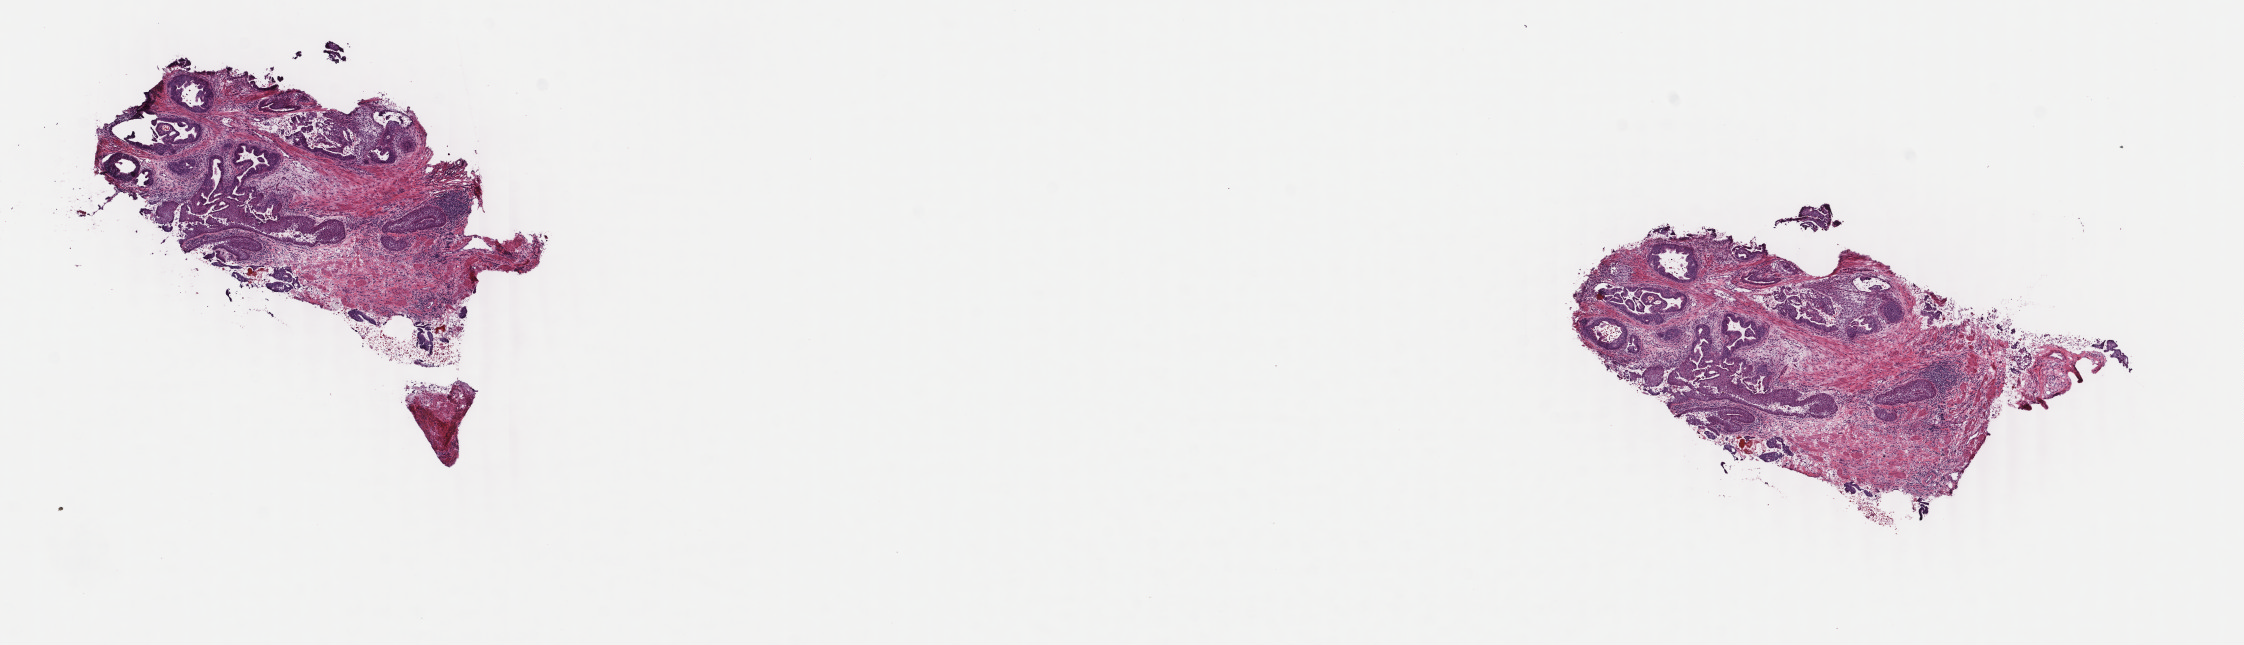
Digitized H&E-stained tissue section (whole slide) — a low-resolution overview of the entire scanned area, about 17.8 x 5.1 mm; frozen section; esophagus, primary tumour sample. Male patient; age at initial diagnosis 76 years. Histologic grade: G2 (moderately differentiated). Pathologist review of this section (percent, as recorded): tumour cells 35%, tumour nuclei 75%, normal cells 0%, stromal cells 60%, necrosis 5%. Infiltration values recorded for this section: lymphocyte infiltration 8%, monocyte infiltration 2%, neutrophil infiltration 2%.
* AJCC pathologic stage: IIIA (7th edition)
* lymph nodes positive (case pathology): 2 of 16 examined
* histologic diagnosis: Adenocarcinoma, NOS (lower third of esophagus)
* TNM: T3 N1 MX